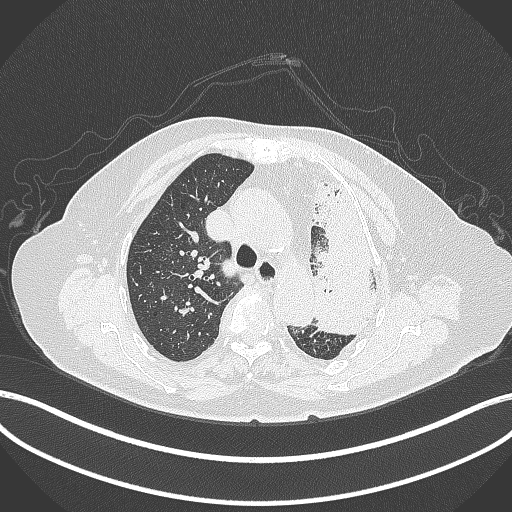
Chest CT, one axial slice. Position 285 of 399 along the scan axis. Lung window (W 1500 / L -600 HU). 1 mm slice thickness. 512 × 512 image matrix, field of view 400 × 400 mm. Patient: female, 75 years. Case-level facts recorded for this patient, not image findings: clinical TNM (as recorded): T3 N3 M1.
Annotated regions visible in this slice (bounding box drawn by a radiologist):
- lung tumour (recorded histology: adenocarcinoma): bounding box [x1, y1, x2, y2] px = [302, 163, 385, 339]